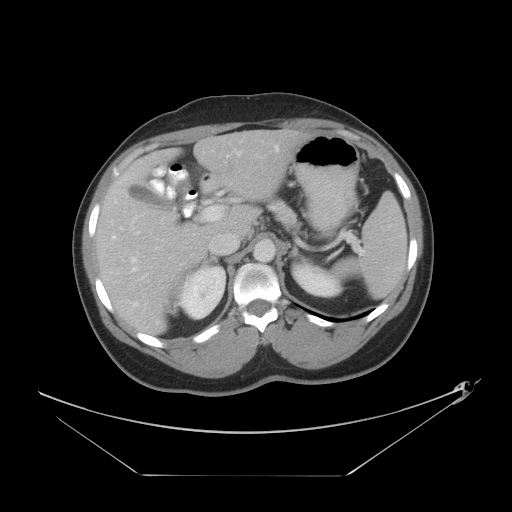
Contrast-enhanced abdominal CT, one axial slice. Slice 26 of 44 in the series (ordered by position). 120 kVp. Intravenous contrast given. Soft-tissue window (W 400 / L 40 HU). 5 mm slice thickness. 512 × 512 image matrix, field of view 466 × 466 mm. Male patient, age 49 years. Case-level facts recorded for this patient, not image findings: diagnosis: colorectal cancer liver metastases, imaged before liver resection; multiple liver metastases: no; largest metastasis: 8.5 cm; disease in both lobes: yes.
Outlined on this slice (manually delineated by an expert):
- hepatic veins: bounding box <131,145,279,262> (left, top, right, bottom; pixels)
- liver: <96,130,312,336>
- planned liver remnant (the part of the liver to remain after resection): <125,130,313,237>
- portal vein (with intrahepatic branches): <112,206,224,271>
- liver metastasis: <225,162,235,172>